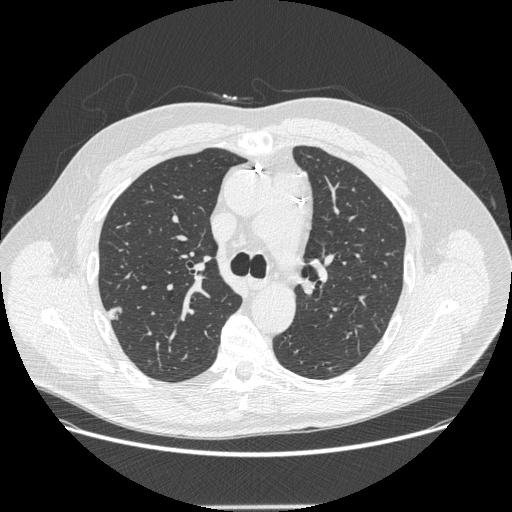
Low-dose screening chest CT, one axial slice. Position 189 of 265 along the scan axis. Lung window (W 1500 / L -600 HU). 1.25 mm slice thickness. 512 × 512 image matrix, field of view 400 × 400 mm.
Outlined on this slice (outlined manually by an expert reader):
- lesion 1 (tumor, upper lobe of right lung): bounding box <107,307,122,321> (left, top, right, bottom; pixels)